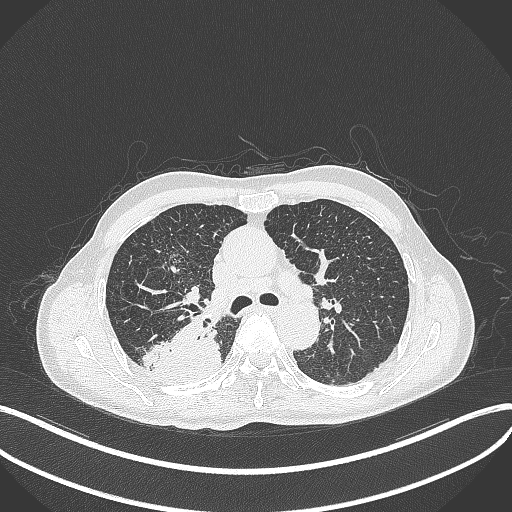
Chest CT, one axial slice; slice 298 of 428 in the series (ordered by position); 120 kVp; lung window (W 1500 / L -600 HU); 1 mm slice thickness; 512 × 512 image matrix, field of view 400 × 400 mm. Patient: male, 79 years. Case-level facts recorded for this patient, not image findings: clinical TNM (as recorded): T3 N0 M0.
Annotated regions visible in this slice (bounding box drawn by a radiologist):
- lung tumour (recorded histology: adenocarcinoma): box from (x=139, y=309) to (x=225, y=382) px